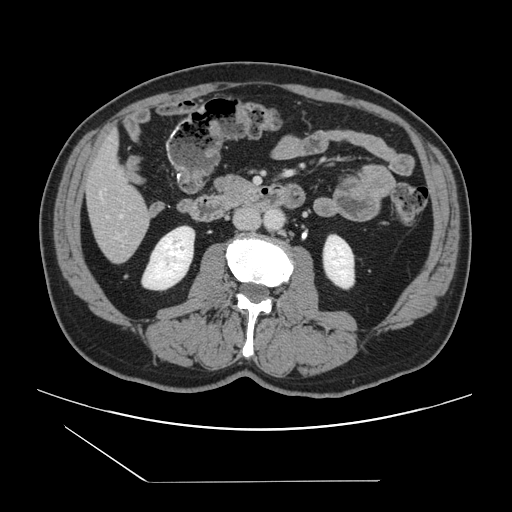
Contrast-enhanced abdominal CT, one axial slice. Slice 36 of 157 in the series (ordered by position). Intravenous contrast given. Soft-tissue window (W 400 / L 40 HU). 2.5 mm slice thickness. 512 × 512 image matrix, field of view 407 × 407 mm. Male patient, age 61 years. Case-level facts recorded for this patient, not image findings: diagnosis: colorectal cancer liver metastases, imaged before liver resection.
Outlined on this slice (expert manual segmentation):
- hepatic veins: bounding box [x1, y1, x2, y2] px = [120, 214, 123, 217]
- liver: [85, 137, 151, 262]
- planned liver remnant (the part of the liver to remain after resection): [85, 136, 147, 219]